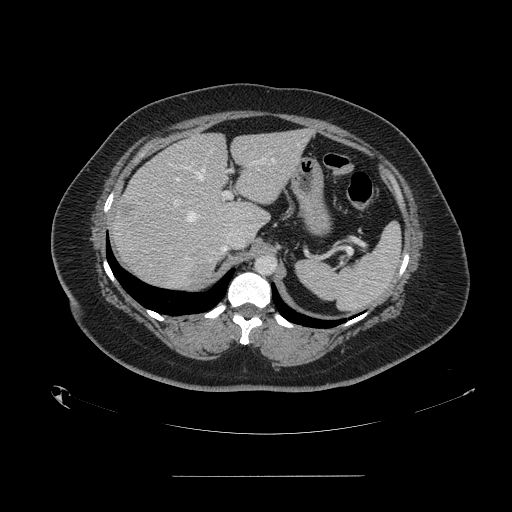
Contrast-enhanced abdominal CT, one axial slice; slice 105 of 164 in the series (ordered by position); intravenous contrast given; soft-tissue window (W 400 / L 40 HU); 2.5 mm slice thickness; 512 × 512 image matrix, field of view 495 × 495 mm. Female patient, age 52 years. From the clinical record (not read from this slice): diagnosis: colorectal cancer liver metastases, imaged before liver resection; multiple liver metastases: yes.
Outlined on this slice (manually delineated by an expert):
- hepatic veins: bounding box <186,144,298,222> (left, top, right, bottom; pixels)
- liver: <112,131,309,290>
- planned liver remnant (the part of the liver to remain after resection): <174,130,309,230>
- portal vein (with intrahepatic branches): <173,158,264,207>
- liver metastasis: <192,265,211,281>
- liver metastasis: <250,210,261,220>
- liver metastasis: <121,203,132,219>